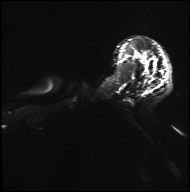
Breast MRI, one axial slice. Position 29 of 36 along the scan axis. Diffusion-weighted series; image 2 of 4 stored at this slice position (different b-values; order by instance number). 3 T. 4 mm slice thickness. 190 × 192 image matrix, field of view 317 × 320 mm. Female patient.
Outlined on this slice (manually delineated by an expert):
- tumour on diffusion-weighted imaging: bounding box [x1, y1, x2, y2] px = [19, 50, 46, 65]